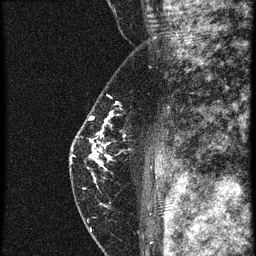
Breast MRI (dynamic contrast-enhanced), one sagittal slice; slice 39 of 60 in the series (ordered by position); 4 images stored at this slice position (order not interpretable as contrast timing); 1.5 T; TE 4.2 ms, TR 20.4 ms; 256 × 256 image matrix. Patient: female, 46 years. From the clinical record (not read from this slice): setting: breast cancer imaged before/during neoadjuvant chemotherapy; receptor status: triple-negative.
Outlined on this slice (semi-automatic segmentation, software-assisted and operator-edited):
- analysis volume of interest (the breast-tissue region the enhancement analysis was run in; not a lesion): bounding box [x1, y1, x2, y2] px = [69, 82, 156, 201]
- tumour enhancement mask (voxels above the 90 % enhancement threshold inside the analysis volume of interest): [72, 114, 113, 185]